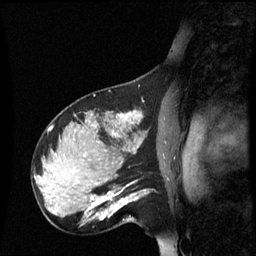
Breast MRI (dynamic contrast-enhanced), one sagittal slice; position 41 of 60 along the scan axis; dynamic contrast-enhanced series, image 2 of 3 at this slice position (ordered by acquisition); 1.5 T; TE 4.2 ms, TR 8.9 ms; 256 × 256 image matrix, field of view 220 × 220 mm. Patient: female, 31 years. From the clinical record (not read from this slice): setting: breast cancer imaged before/during neoadjuvant chemotherapy; receptor status: HR-positive, HER2-negative.
Outlined on this slice (semi-automatic segmentation, software-assisted and operator-edited):
- analysis volume of interest (the breast-tissue region the enhancement analysis was run in; not a lesion): bounding box <90,180,145,223> (left, top, right, bottom; pixels)
- tumour enhancement mask (voxels above the 70 % enhancement threshold inside the analysis volume of interest): <90,186,138,221>